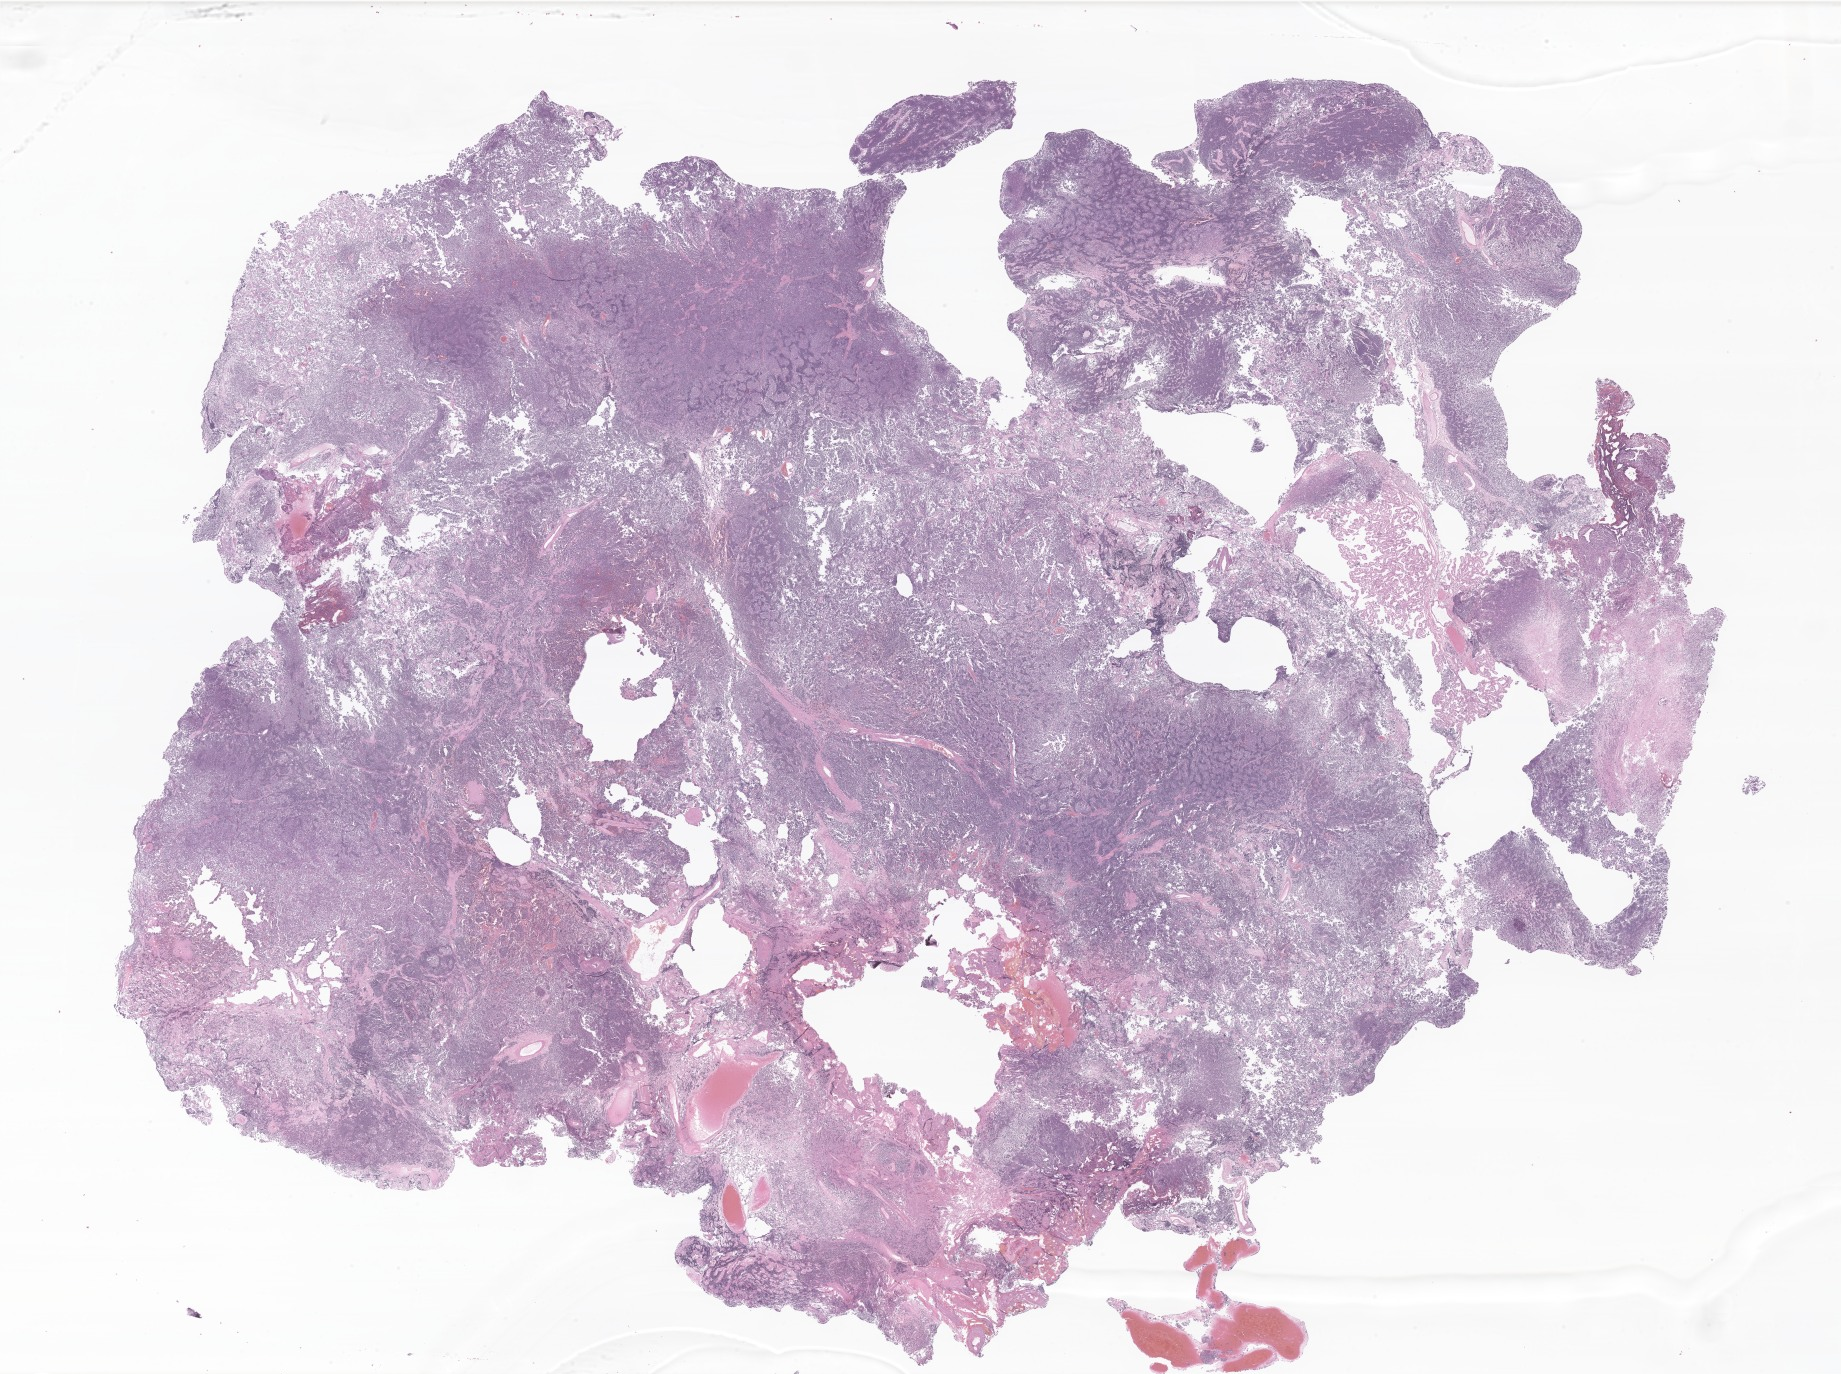
Whole-slide image, H&E stain of tumor tissue from the cerebellum, low-resolution overview of the scanned area, about 31.1 x 23.2 mm; FFPE section. Female patient, age 35 months (2 years 11 months).
* diagnosis: Medulloblastoma, NOS